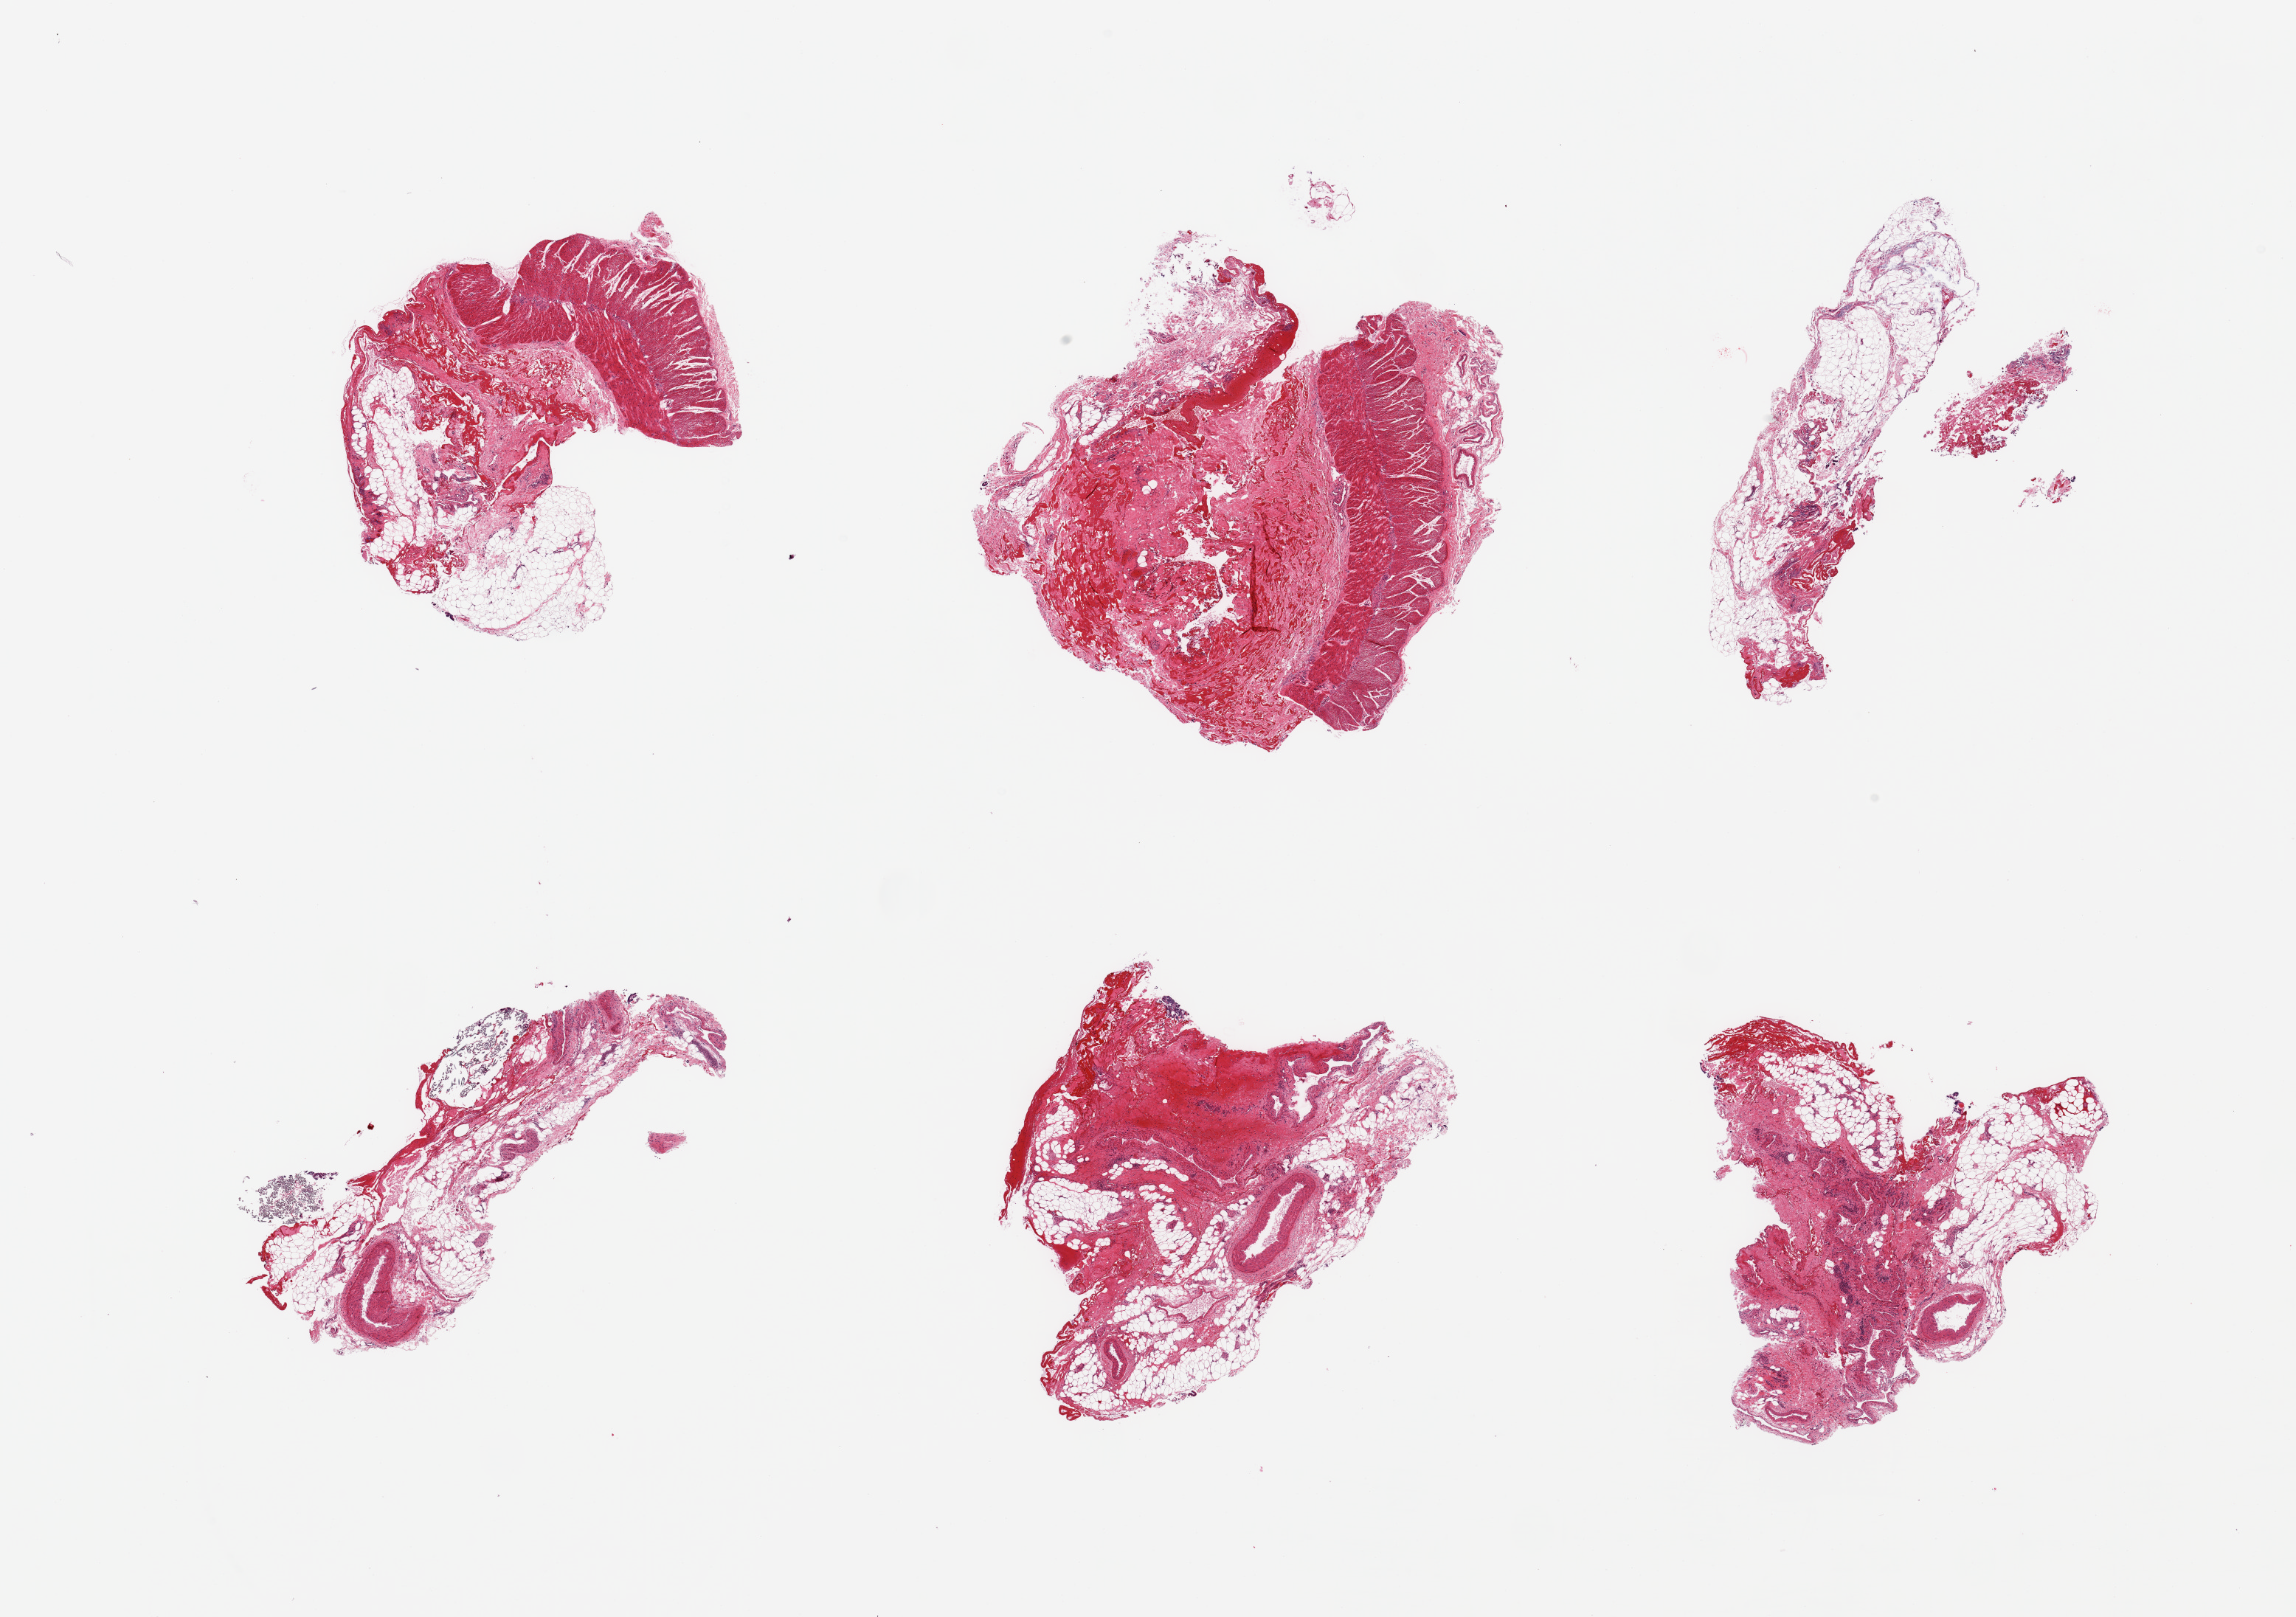
Whole-slide image, haematoxylin and eosin stain — a low-resolution overview of the entire scanned area, about 24.6 x 17.3 mm. PAXgene-fixed, paraffin-embedded tissue. Section of gastroesophageal junction (target tissue). Donor tissue sample. Donor sex: male.
- reviewer comment on this tissue sample: 6 pieces, some target muscularis but mainly (~70%) fibroadipose/vascular elements